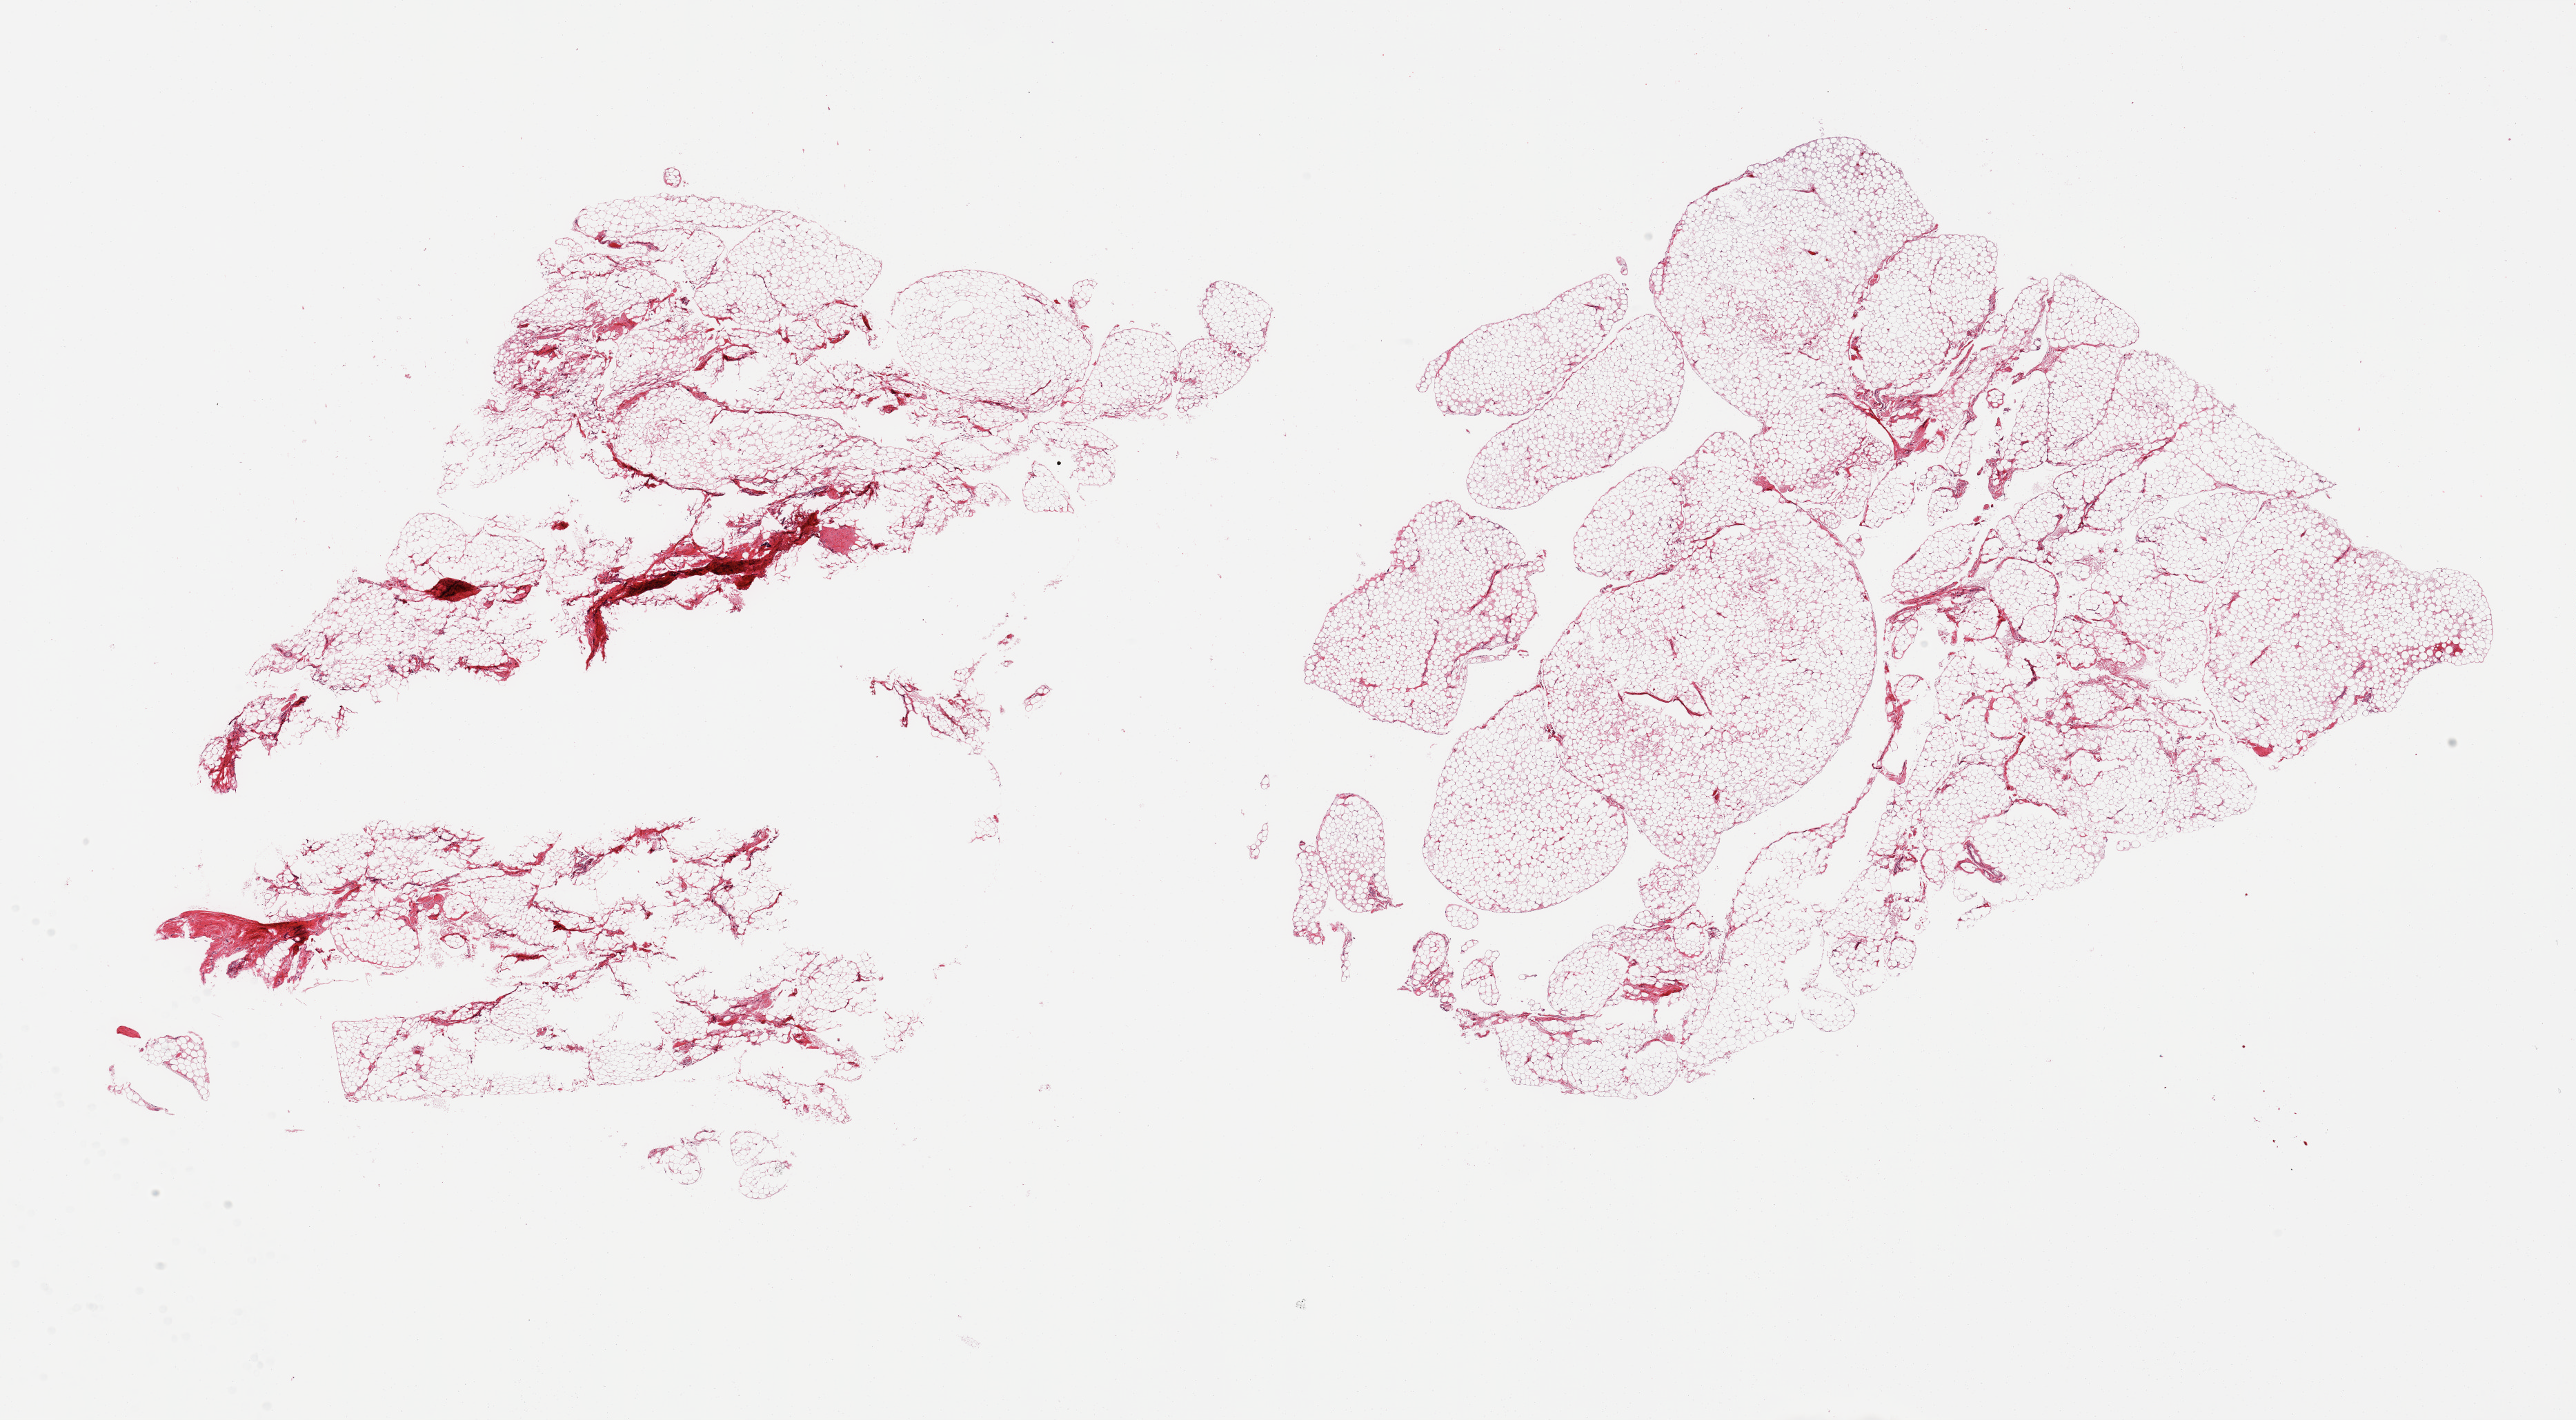
Haematoxylin and eosin whole-slide image, shown as a low-resolution overview of the whole scanned area (about 29.5 x 16.3 mm, slide scanned at 20x); PAXgene-fixed, paraffin-embedded tissue; target tissue: omentum; donor tissue sample. Donor sex: female.
Pathologist's review note for this sample: 2 pieces; lobulated fatty tissue; low fibrous content.